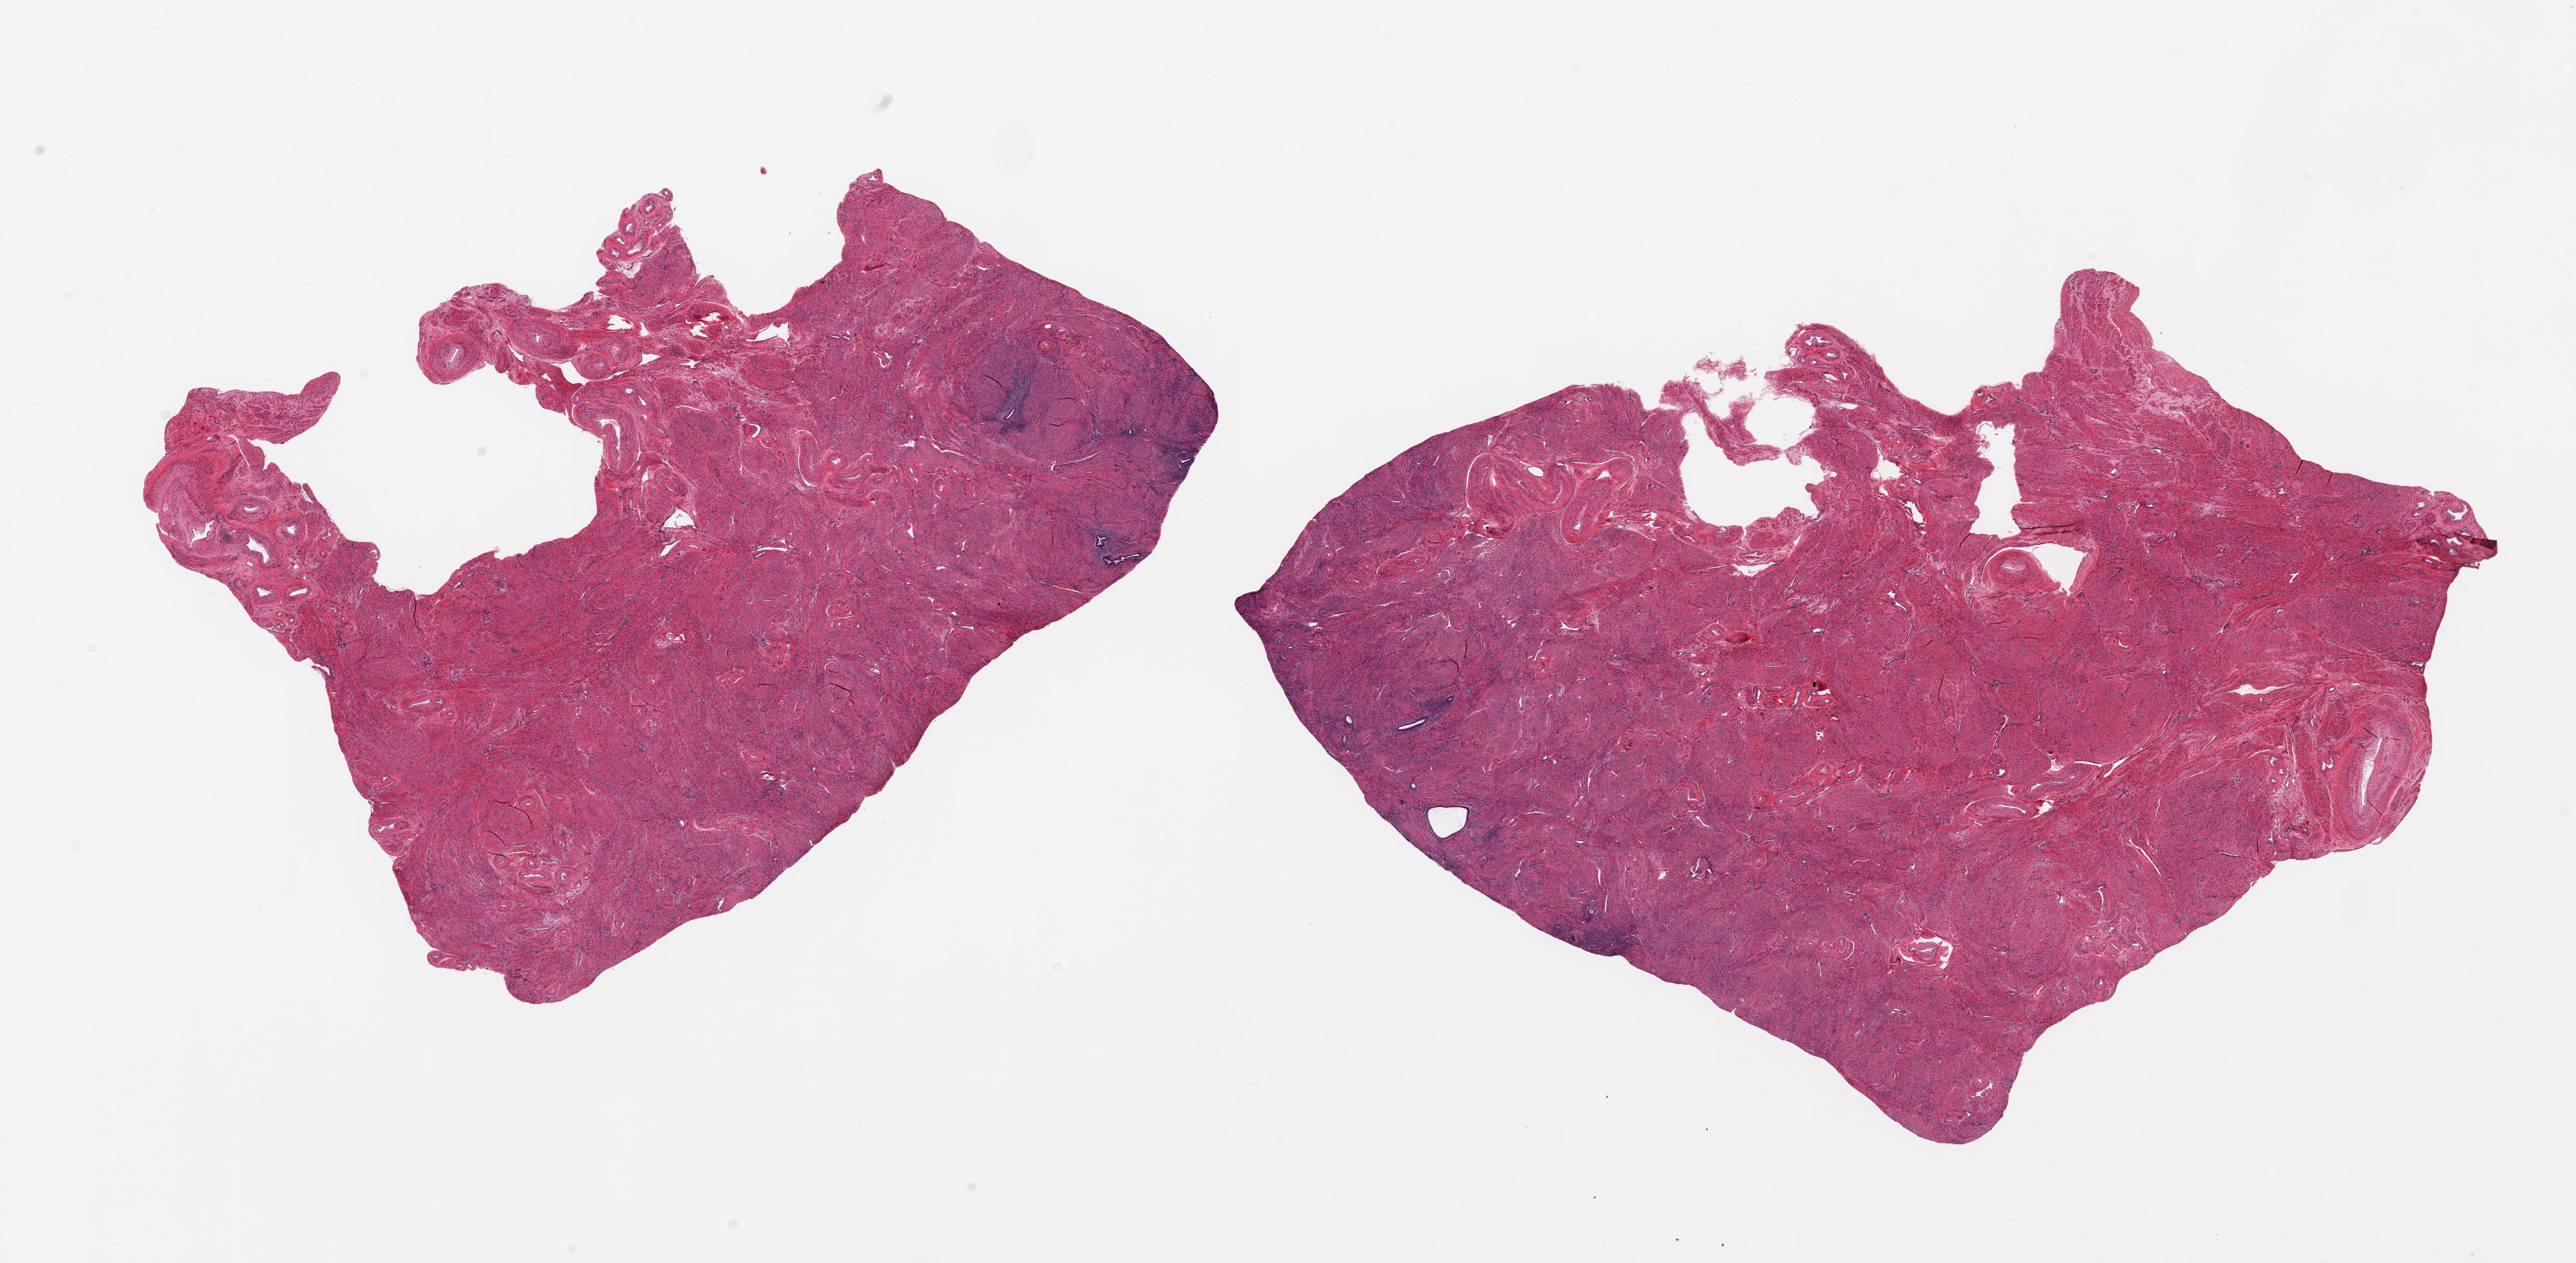
Digitized hematoxylin and eosin (H&E)-stained section, shown as a low-resolution overview of the whole scanned area (about 26.6 x 13.0 mm, from a 20x scan). PAXgene-fixed paraffin-embedded (PFPE) section. Sampled site (target tissue): uterus. Tissue donor sample.
* reviewer comment on this tissue sample: 2 pieces; predominantly myometrium with scant endemetrial component